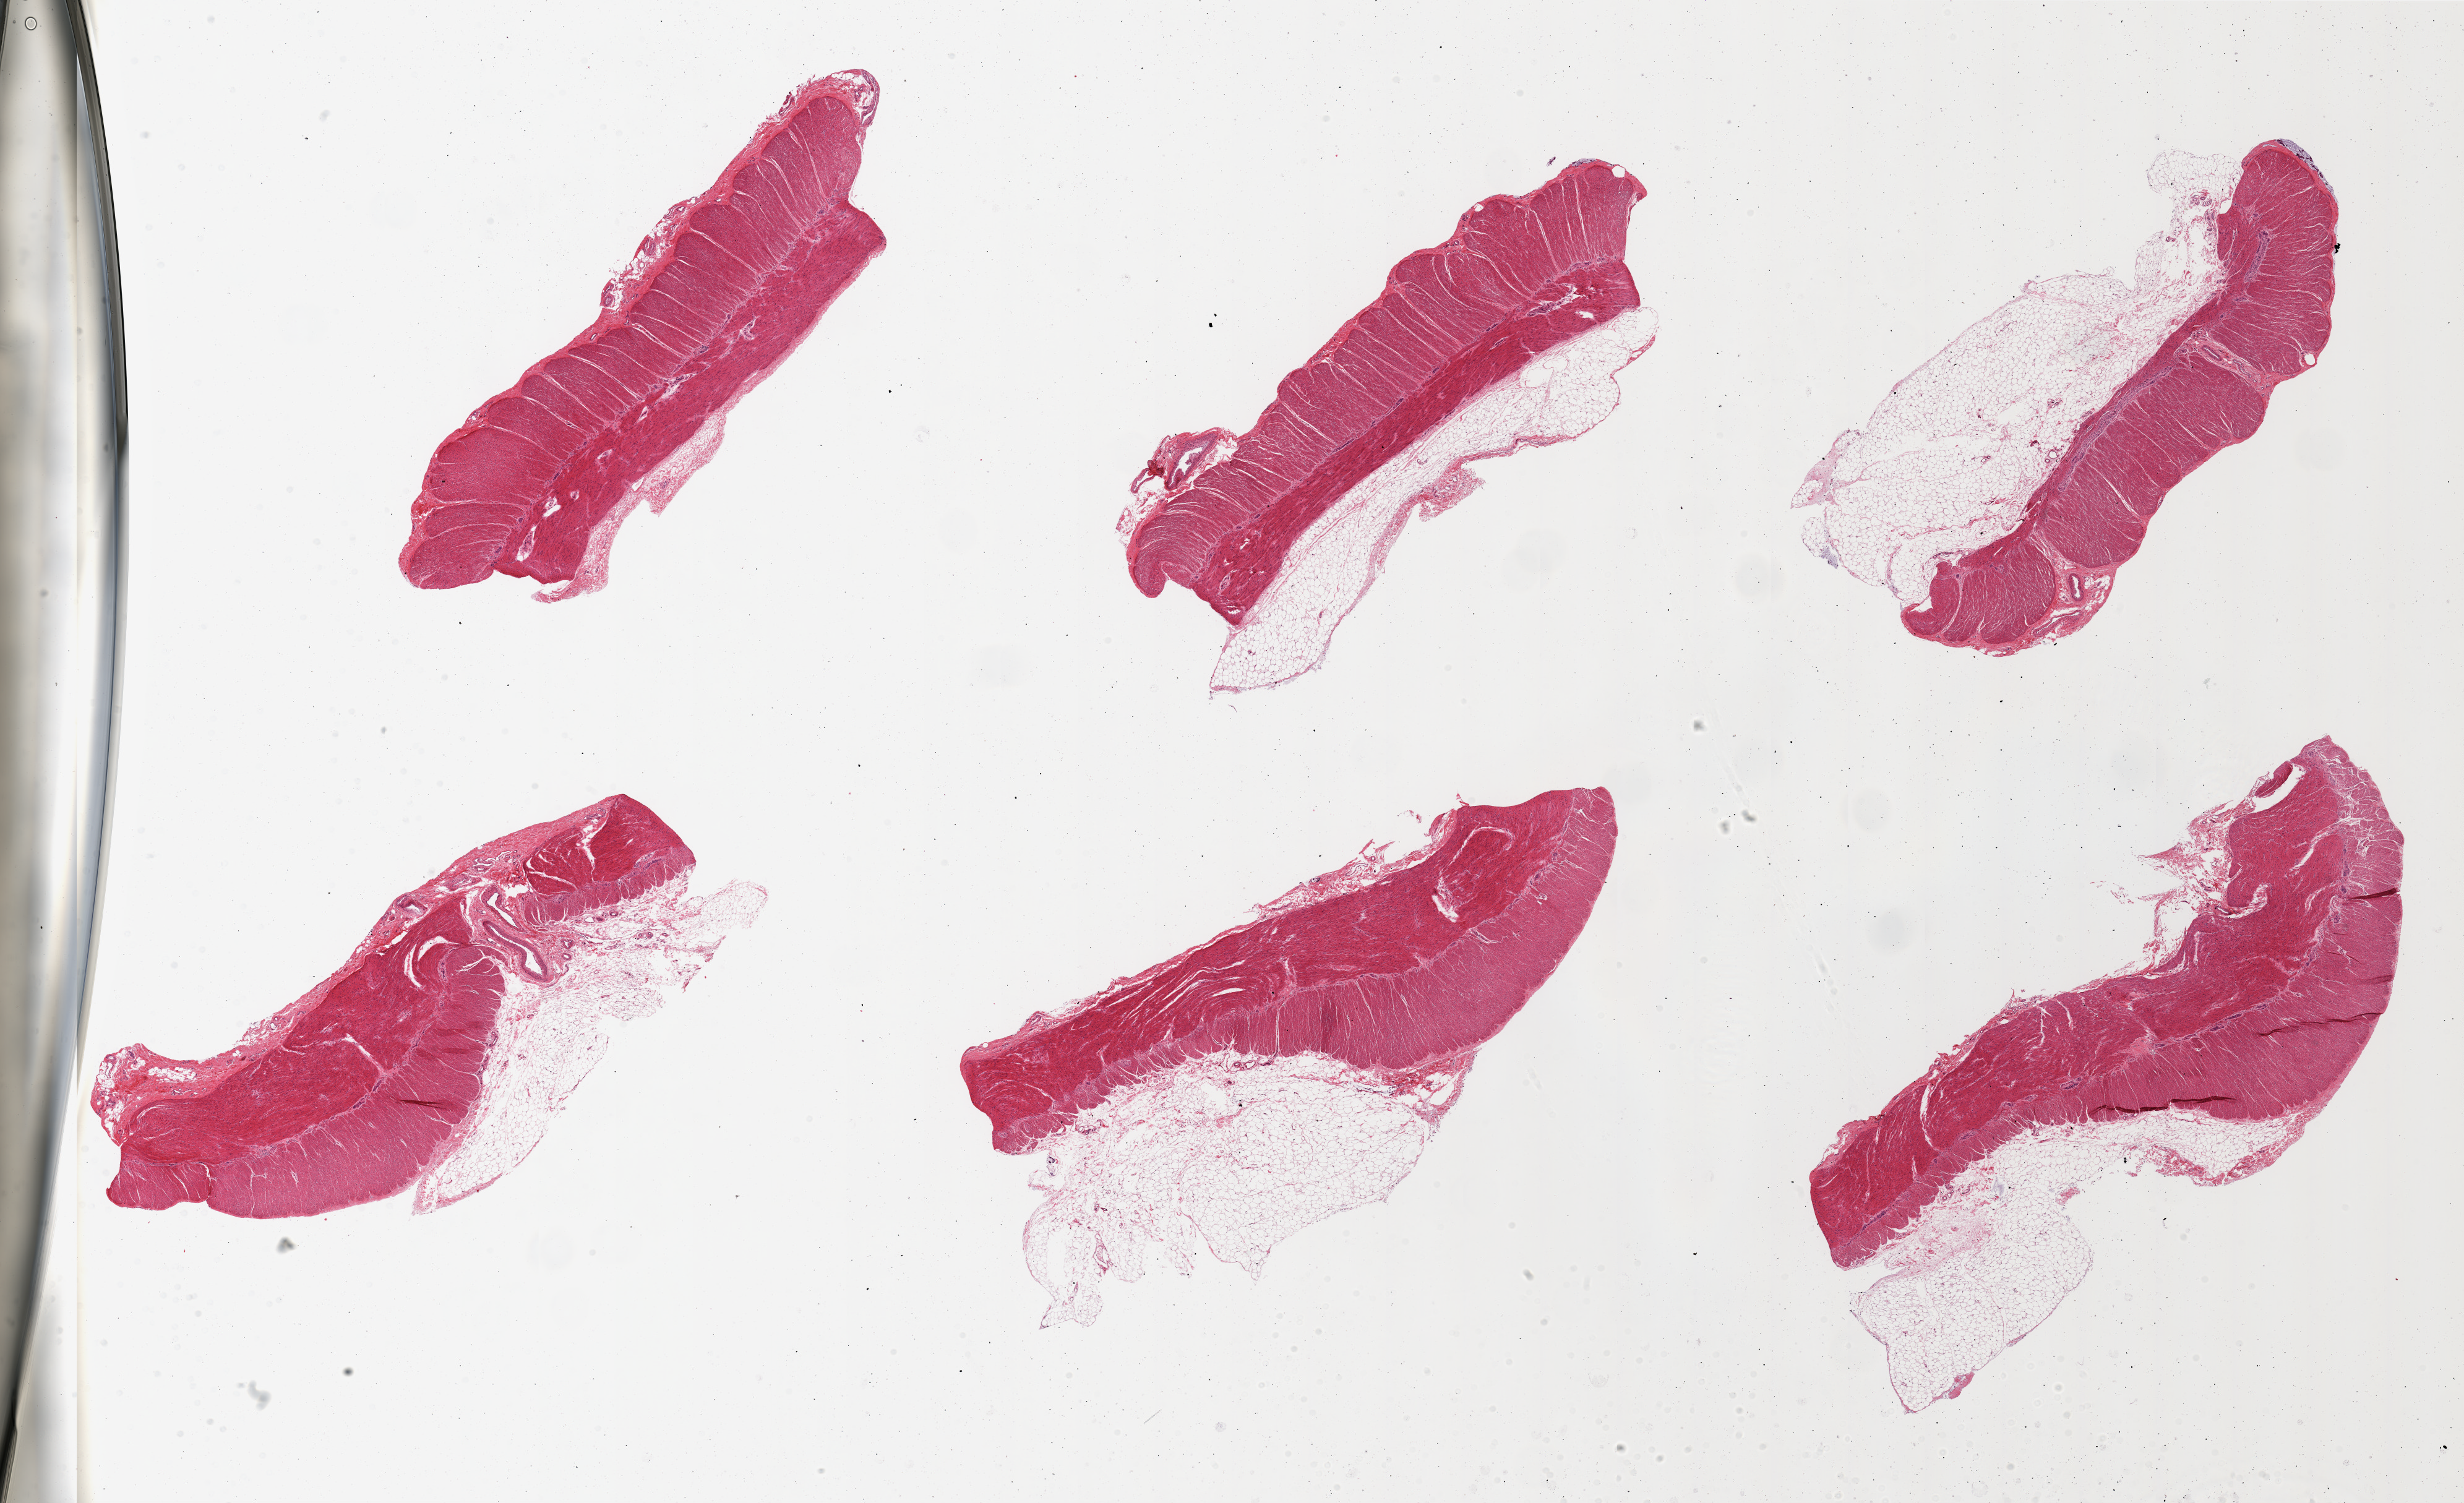
Whole-slide image, hematoxylin and eosin (H&E) stain, shown as a low-resolution overview of the whole scanned area (about 31.5 x 19.2 mm), PAXgene-fixed, paraffin-embedded tissue, section of sigmoid colon (target tissue), donor tissue sample. Female donor.
Review note (as recorded): 6 pieces, muscularis; adherent fat on some sections, up to ~2.5mm.